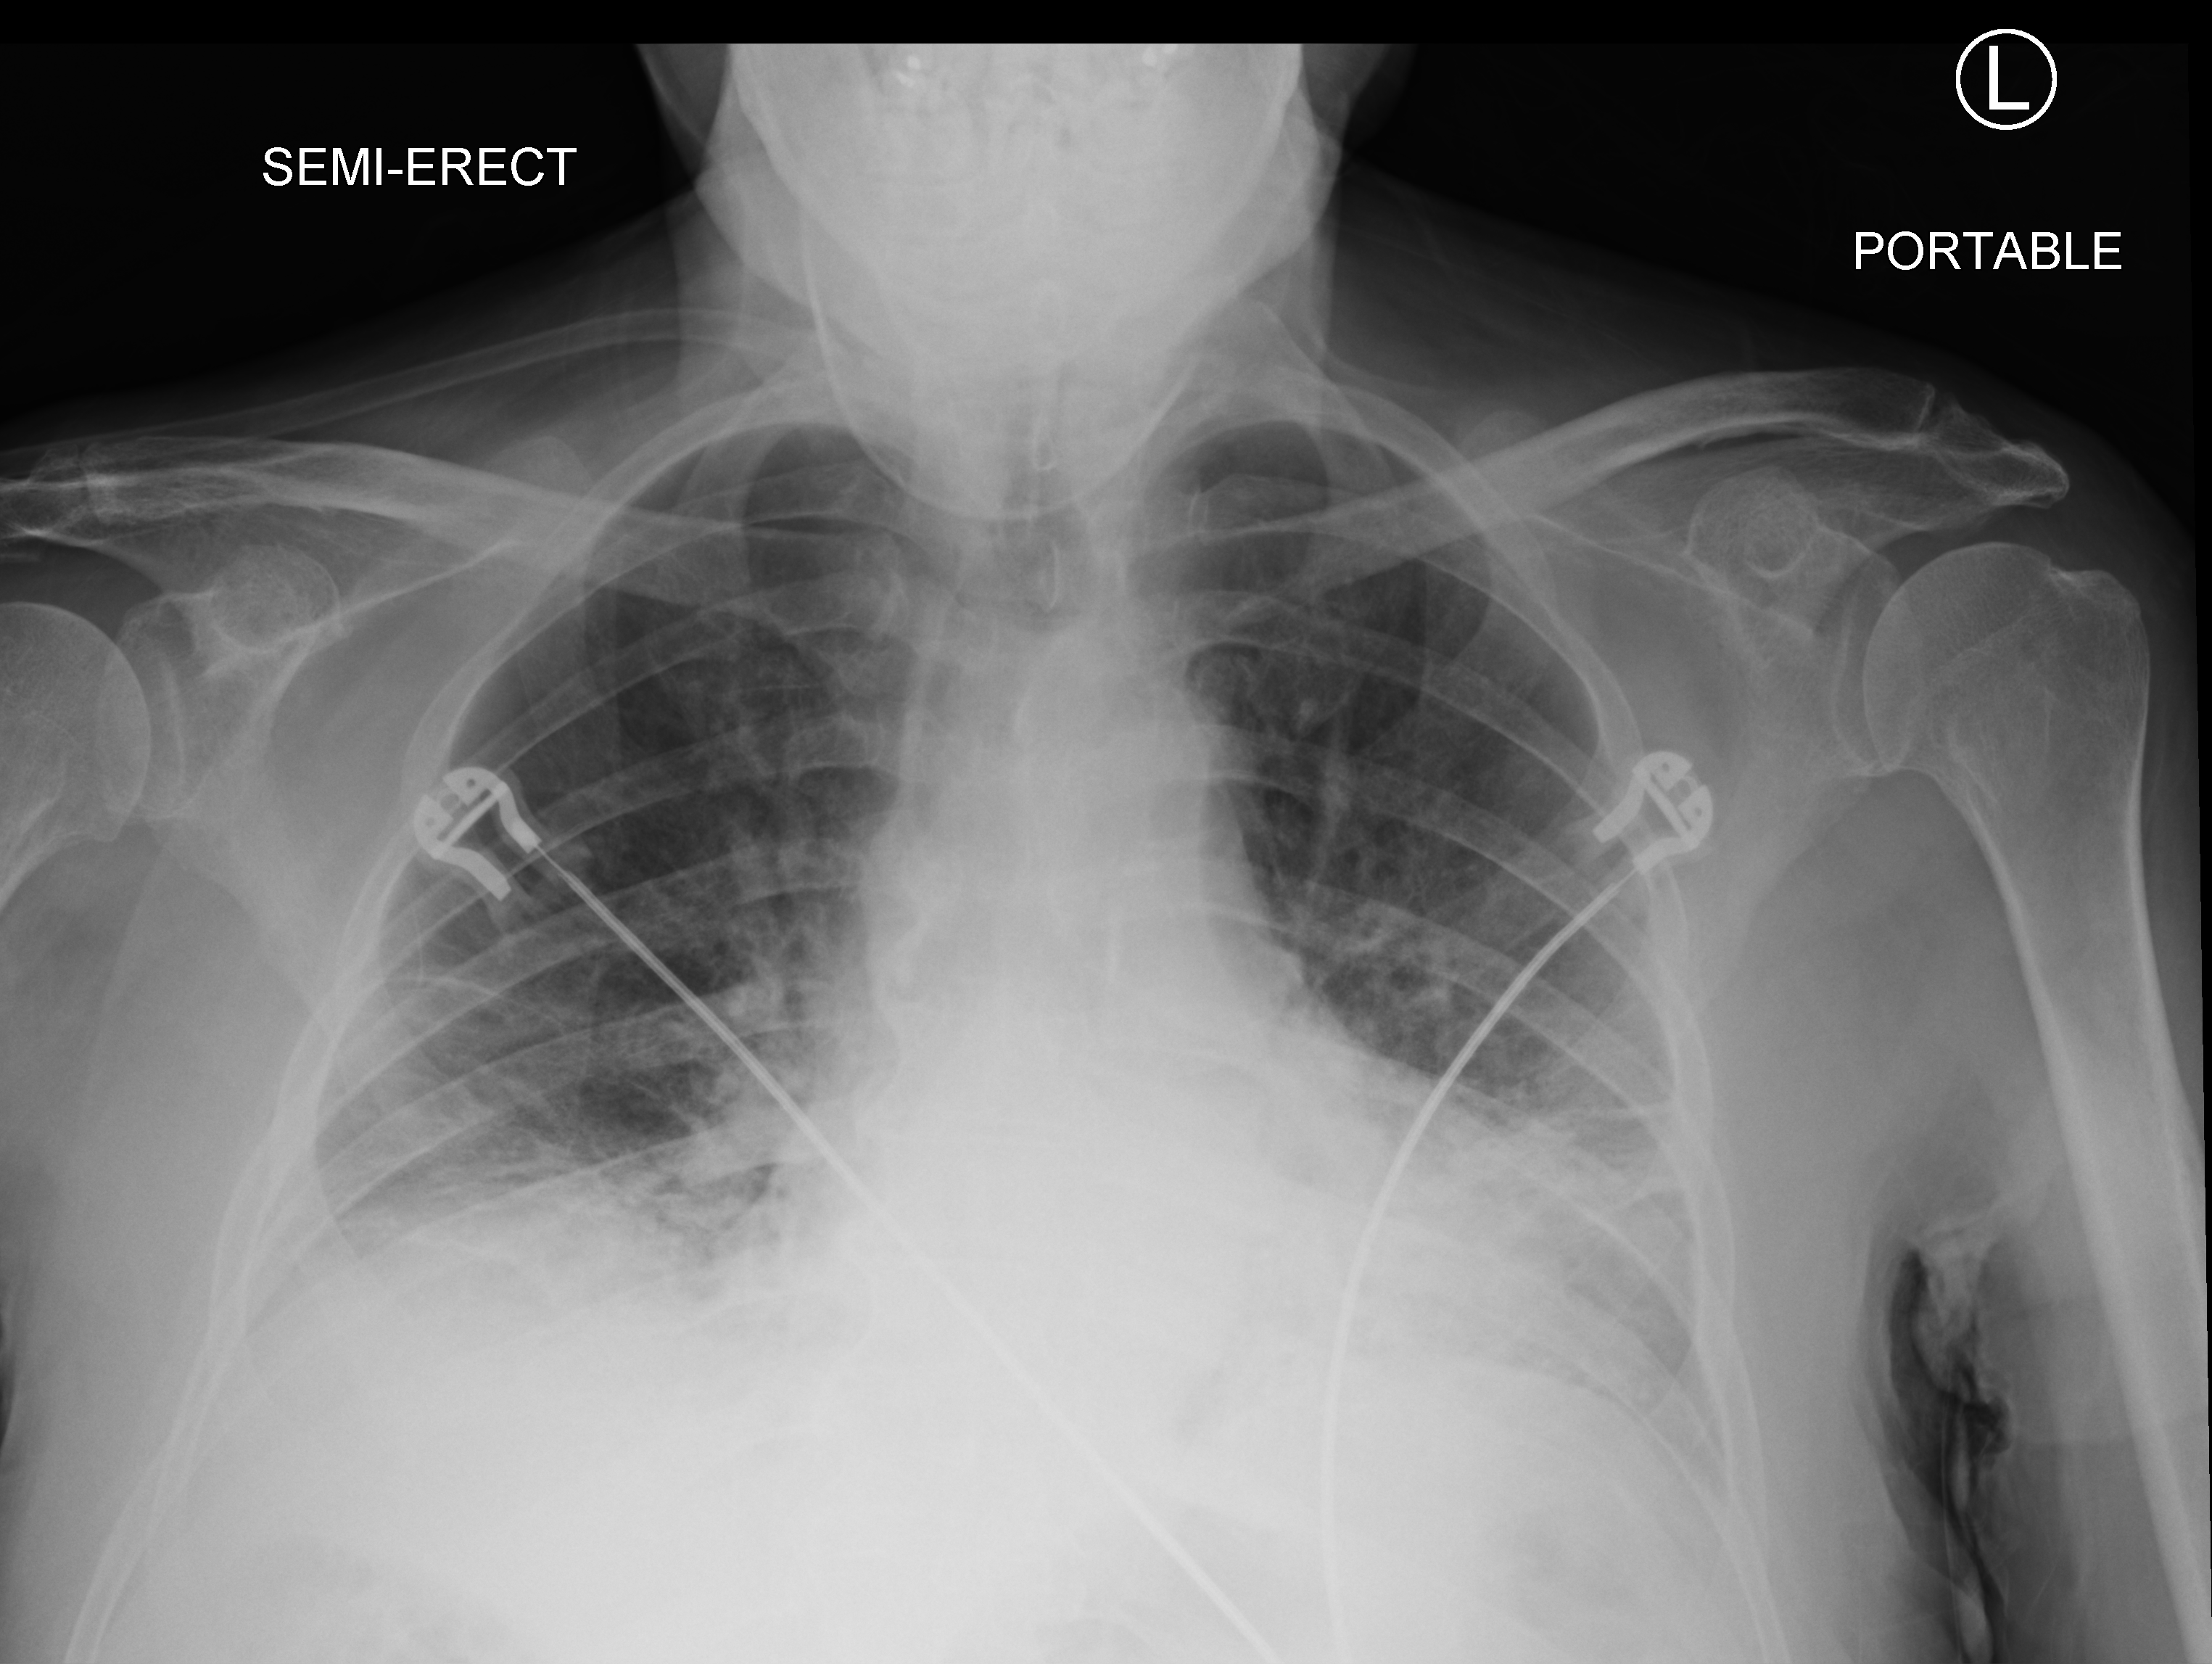
Bedside chest radiograph (computed radiography). Patient hospitalised with COVID-19; male, aged 75–90 years.
From the hospital-stay record, not from the radiograph (when in the stay this image was taken is not recorded): mechanically ventilated during this hospital stay: yes; admitted to intensive care during this hospital stay: yes; smoking status (admission record): never.